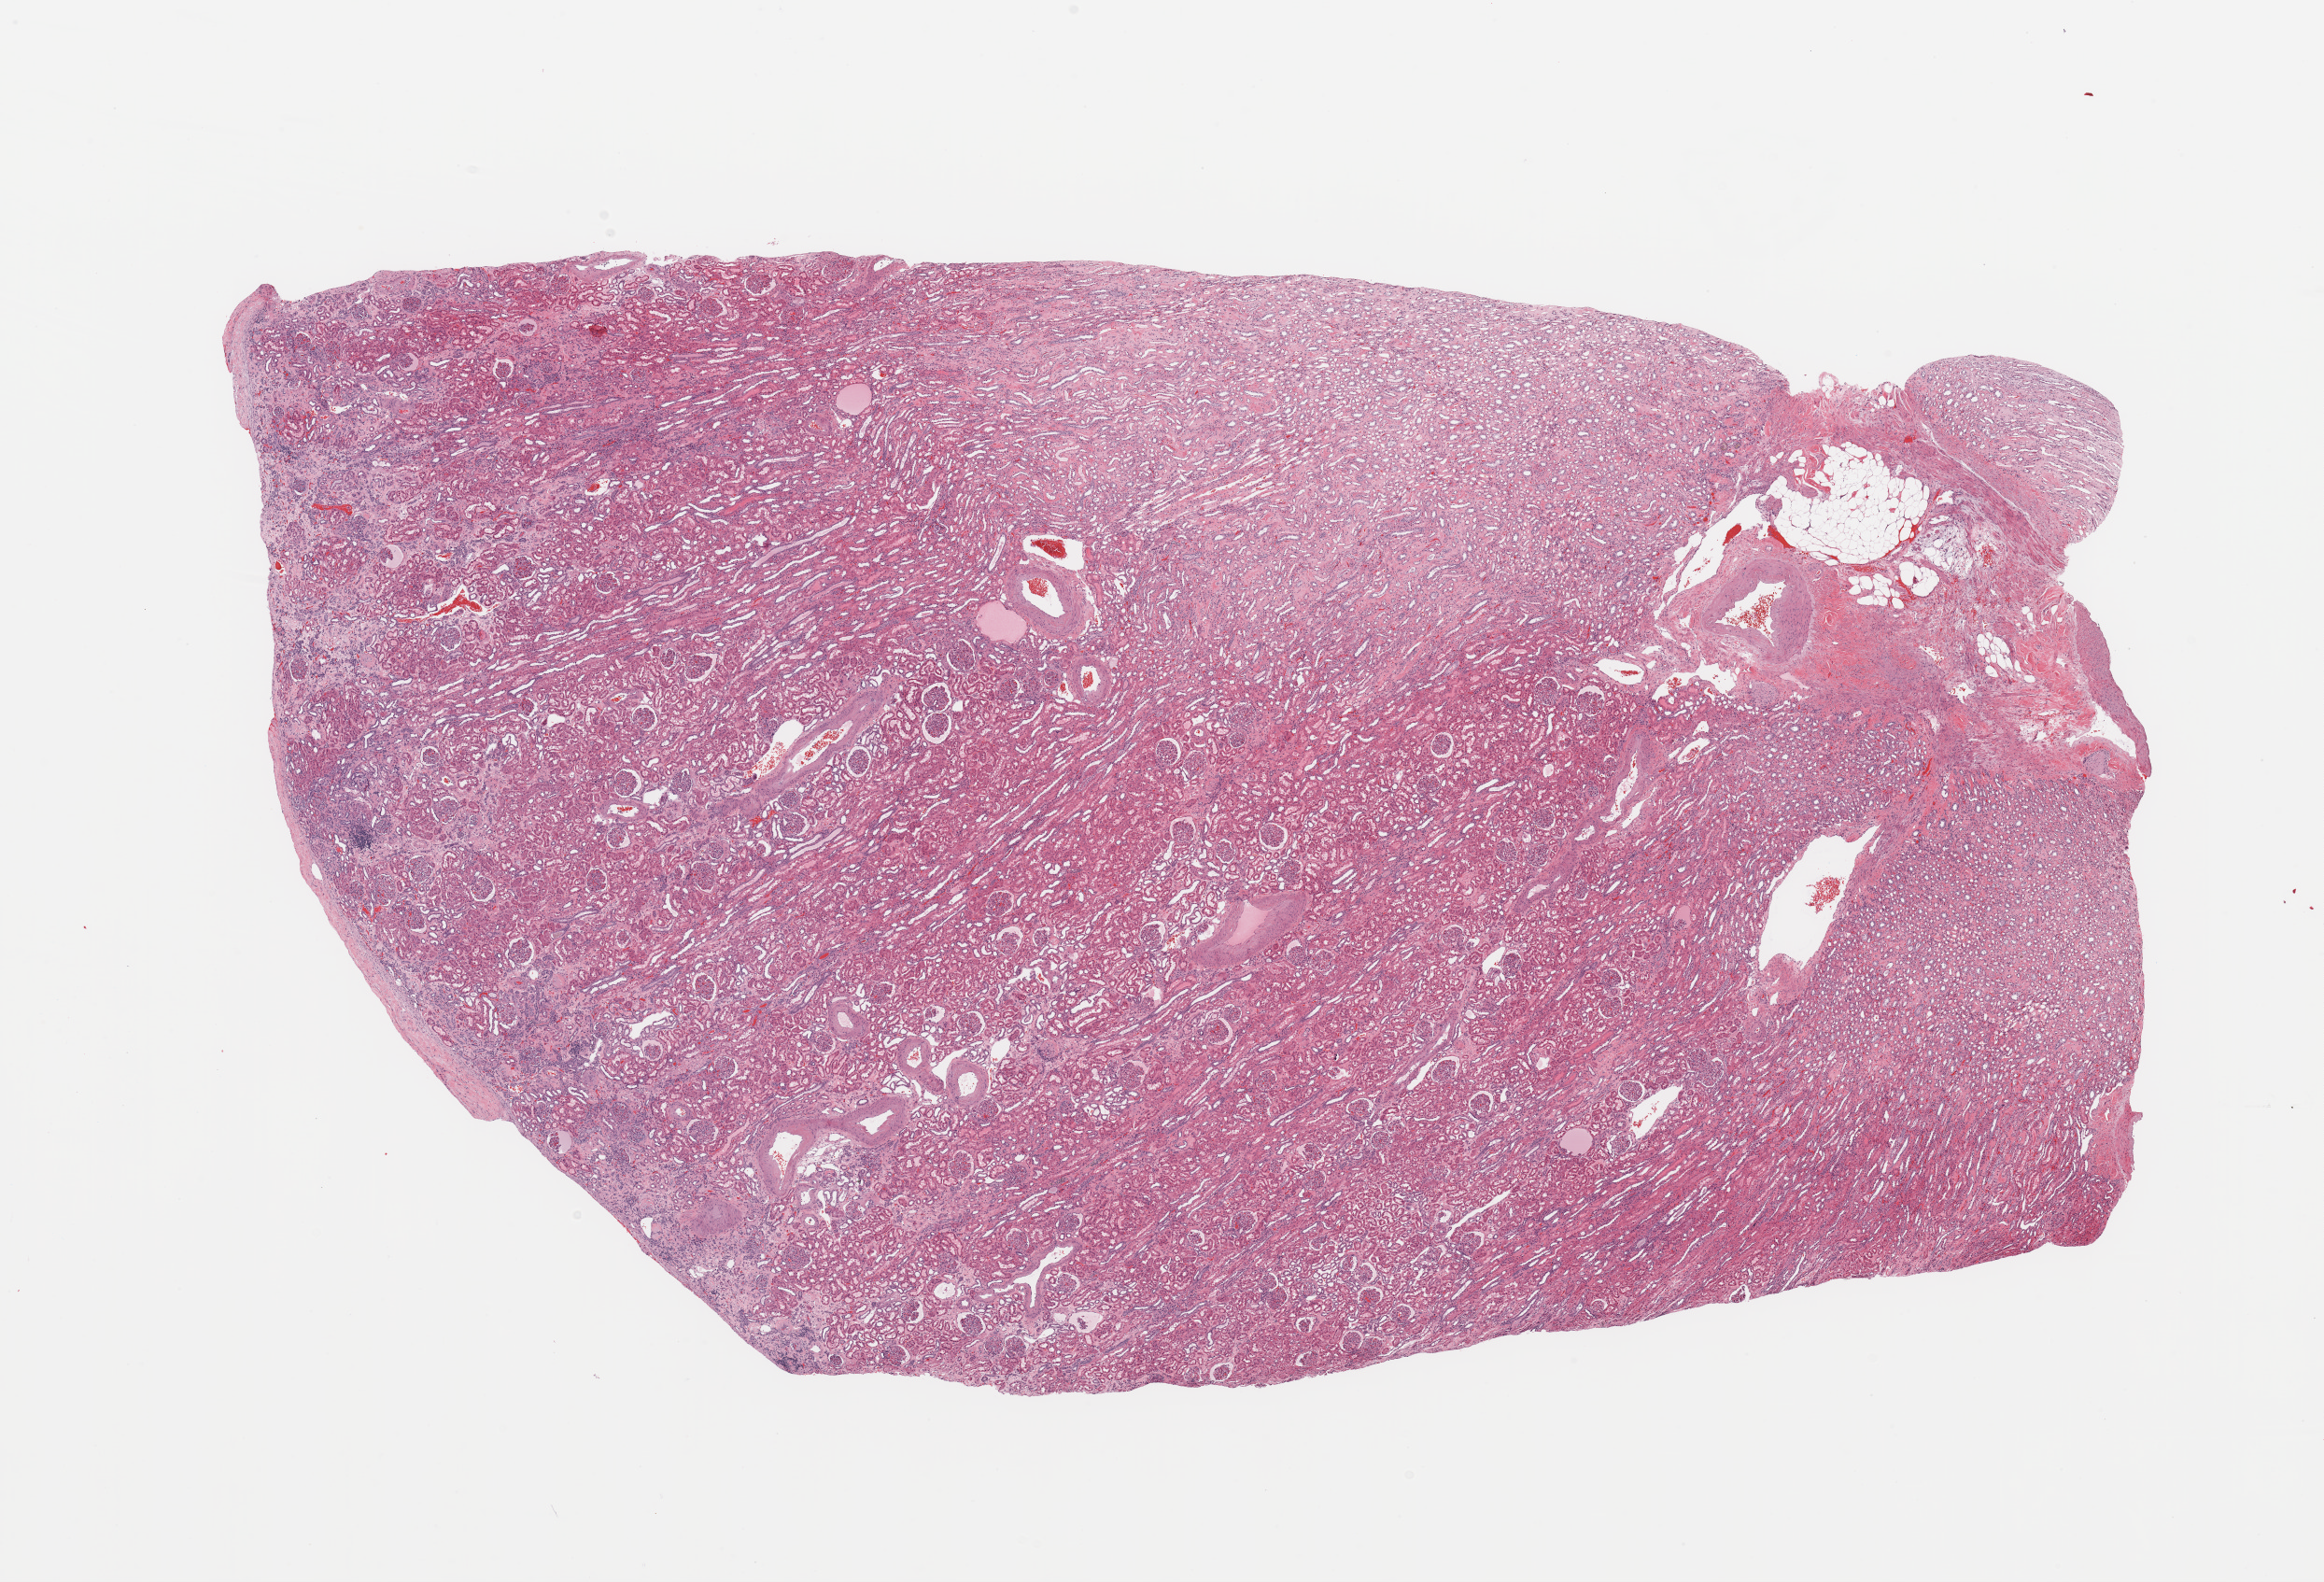
Digitized H&E-stained tissue section (whole slide), whole scanned area (about 19.7 x 13.4 mm, acquisition: 20x scan) shown as a low-resolution overview. Normal (non-tumour) tissue sample, sampled site: kidney. 76-year-old male patient.
This section: normal (non-tumour) tissue from the same patient. Patient diagnosis: Renal cell carcinoma, NOS.